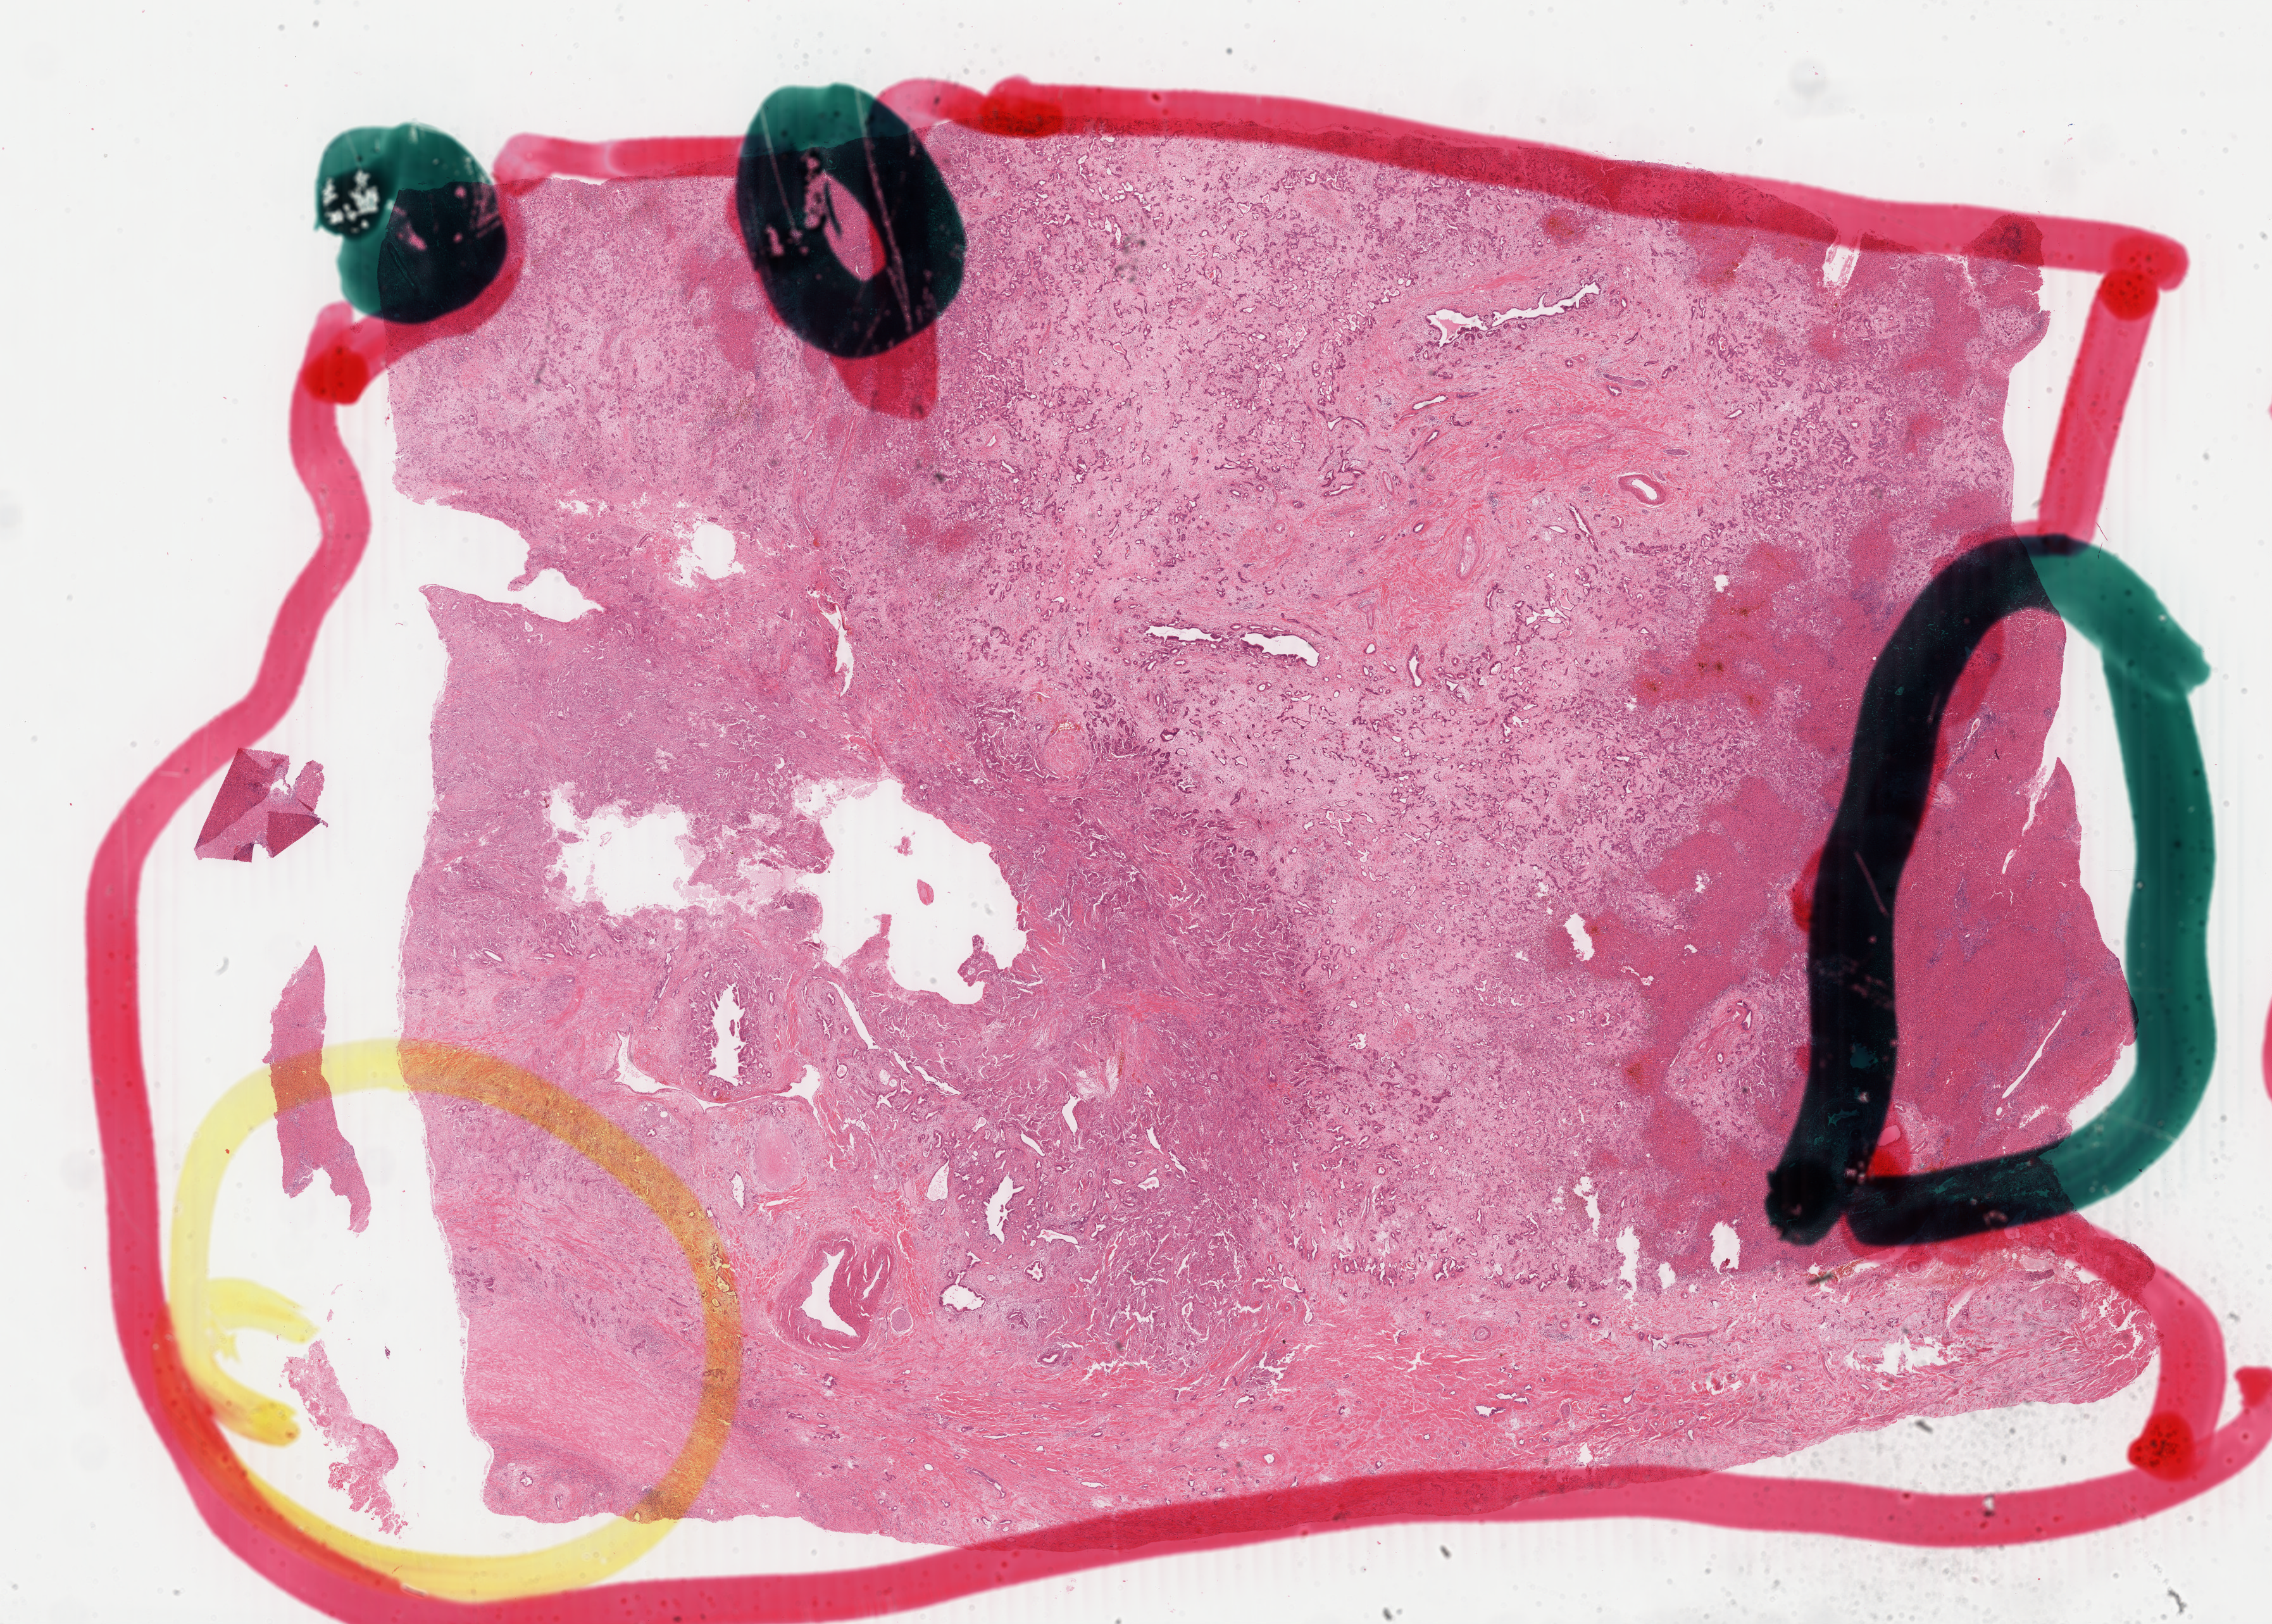
Whole-slide histology image, Hematoxylin and eosin (H&E) stained — shown as a low-resolution overview of the whole scanned area (about 28.6 x 20.4 mm, acquisition: 40x scan). Formalin-fixed paraffin-embedded (FFPE) diagnostic section. Primary tumour sample from the liver. Male, age 54 years at initial diagnosis. Histologic grade: G2 (moderately differentiated).
Histologic diagnosis: Combined hepatocellular carcinoma and cholangiocarcinoma. TNM: T3a N0 M0. AJCC pathologic stage: IIIA.